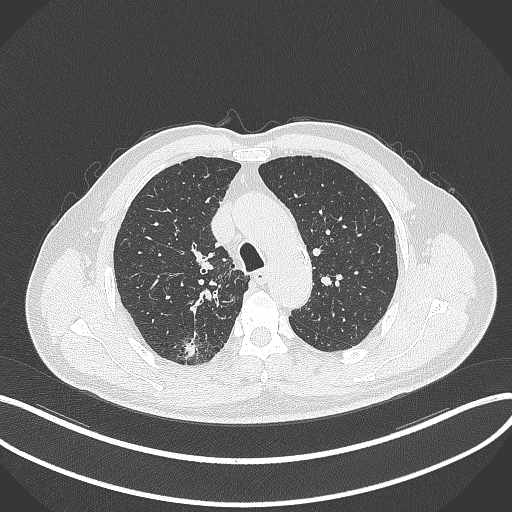
Chest CT, one axial slice. Slice 273 of 359 in the series (ordered by position). Reconstruction kernel B70f. 120 kVp. Lung window (W 1500 / L -600 HU). 1 mm slice thickness. 512 × 512 image matrix. Male patient, age 69 years. From the clinical record (not read from this slice): clinical TNM (as recorded): T1b N0 M0; histopathological grade: G2-3.
Structures marked on this image (rectangle marked by the reading radiologist):
- lung tumour (recorded histology: adenocarcinoma): box from (x=180, y=336) to (x=199, y=361) px